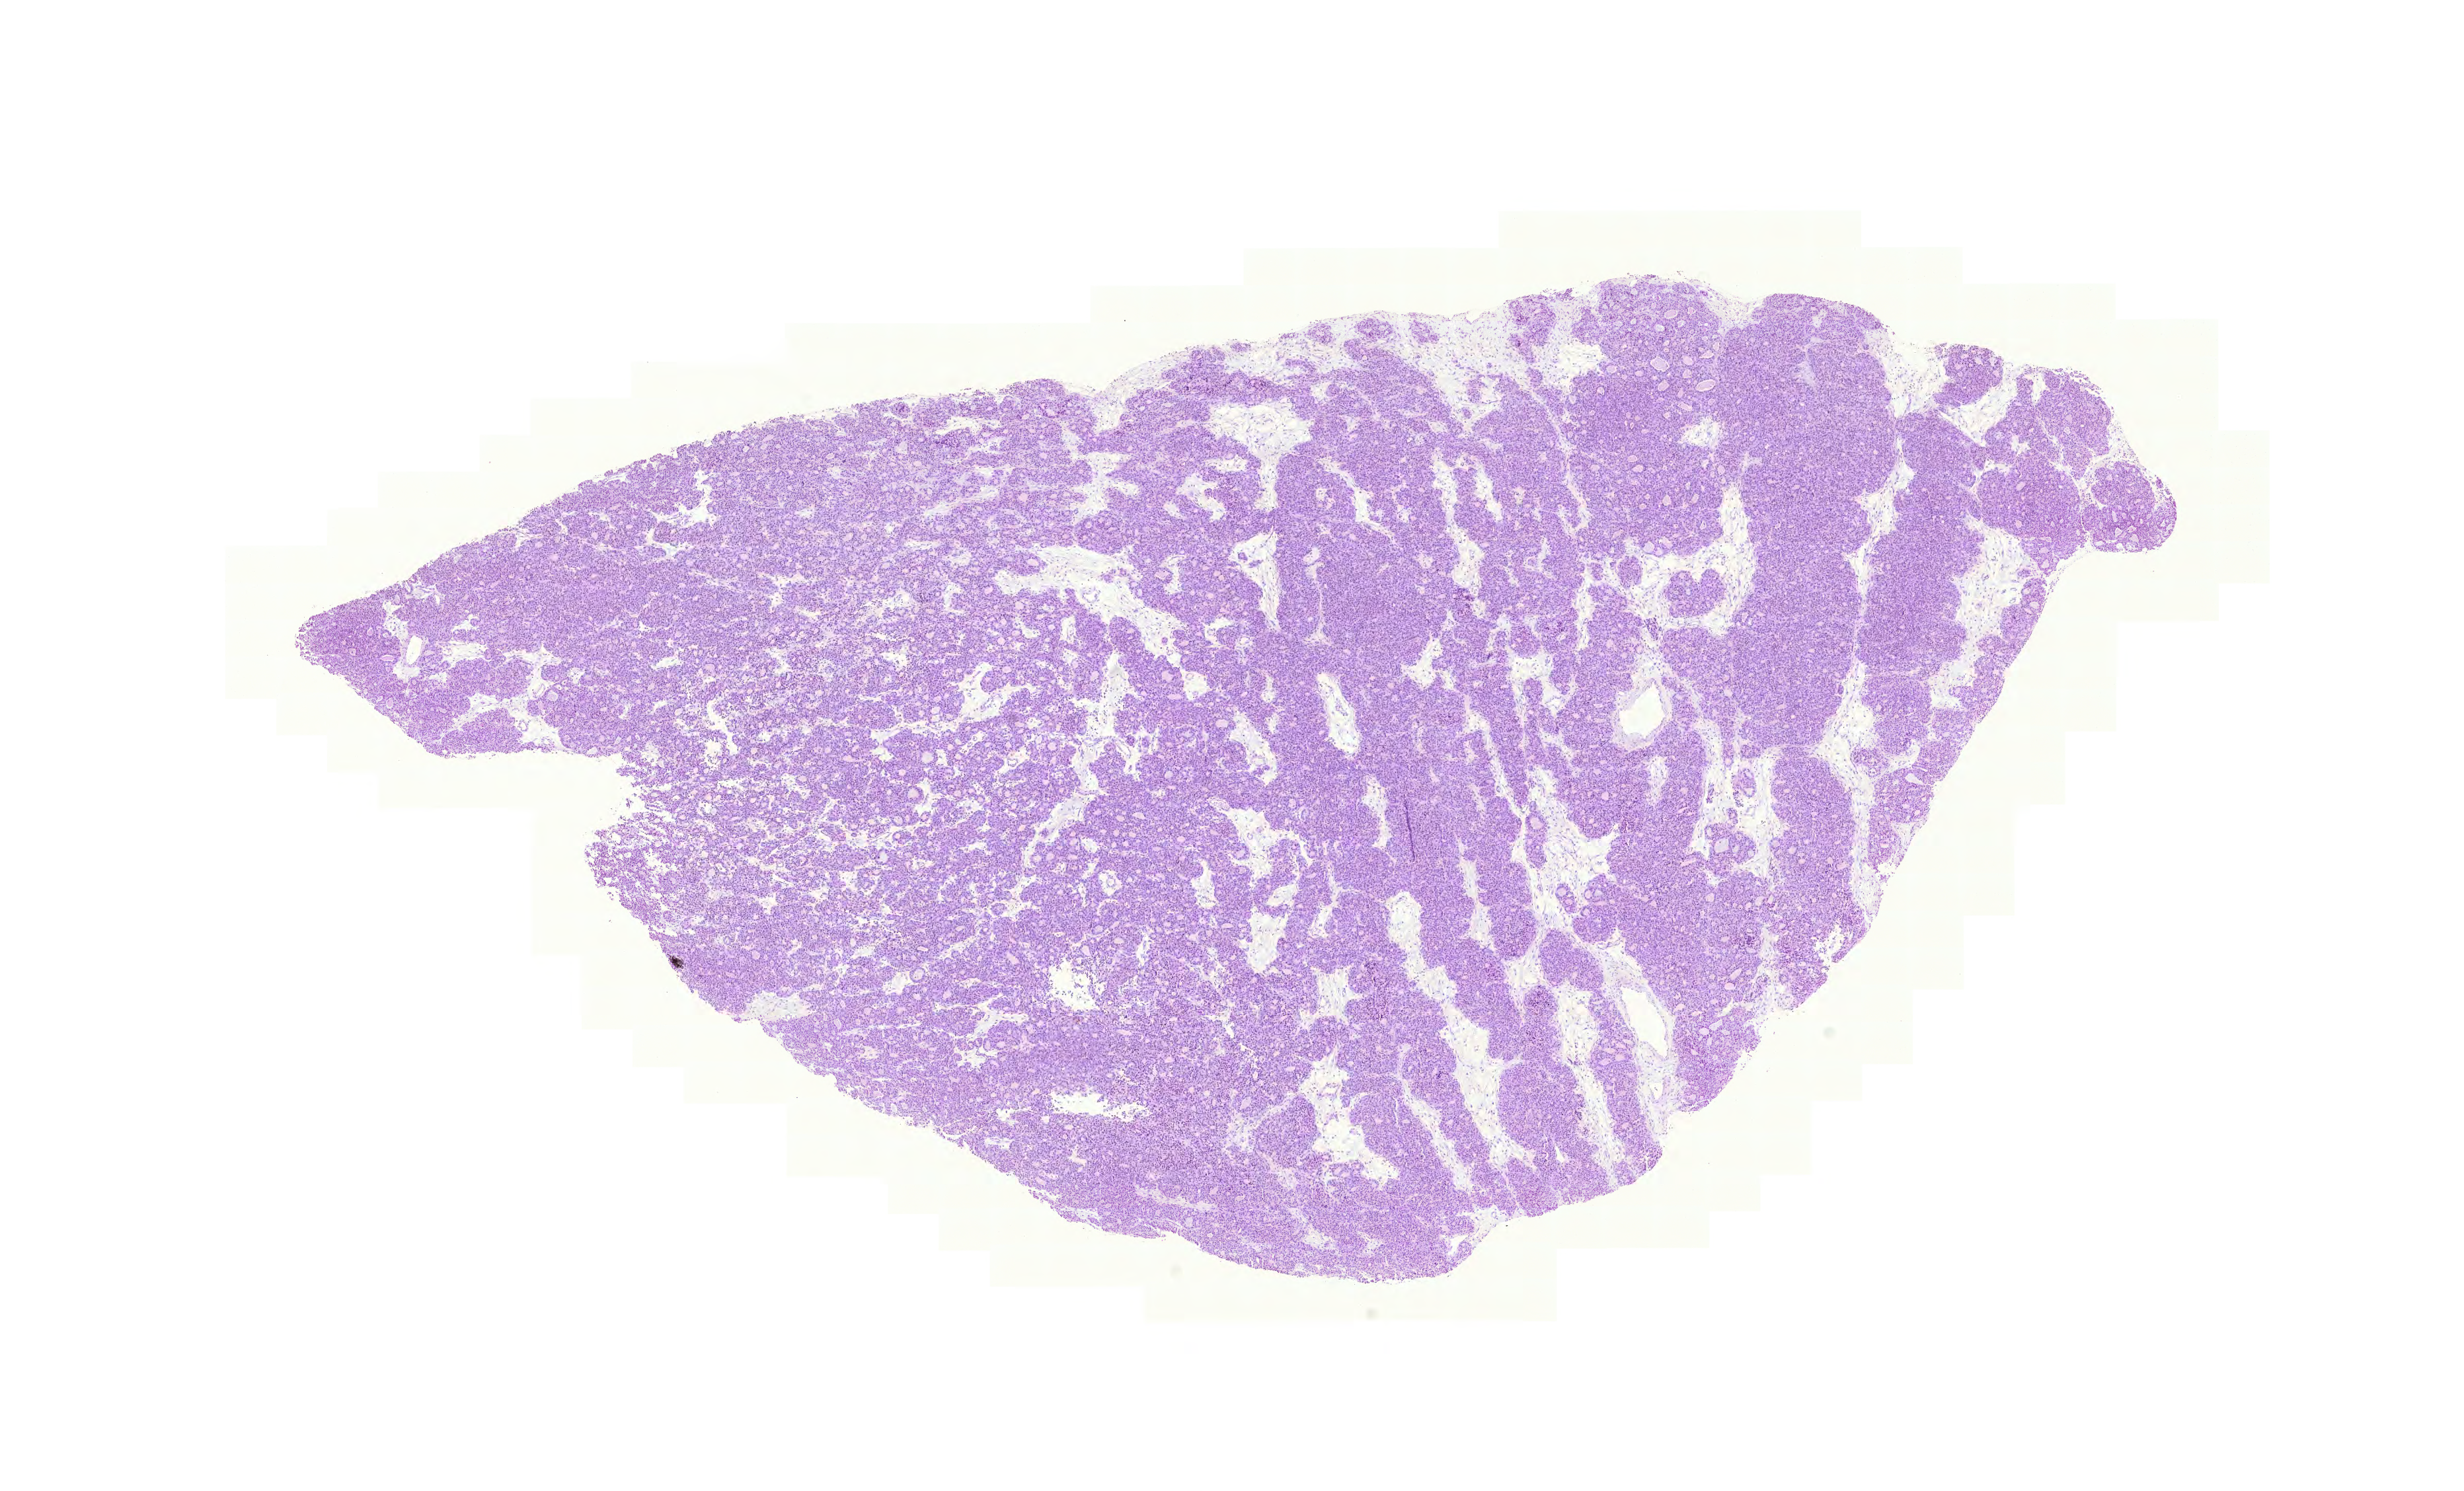
Hematoxylin and eosin (H&E) stained whole-slide image, shown as a low-resolution overview of the whole scanned area (about 13.9 x 8.4 mm), formalin-fixed paraffin-embedded (FFPE) diagnostic section, stomach, primary tumour sample. Male patient; age at initial diagnosis 68 years. Histologic grade: G2 (moderately differentiated).
Histologic diagnosis: Adenocarcinoma, intestinal type (body of stomach). AJCC pathologic stage: IA. Lymph nodes positive (case pathology): 0 of 30 examined.